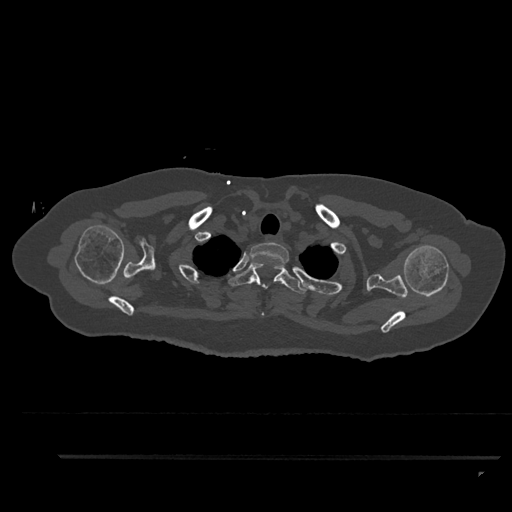
CT including the spine, one axial slice; slice 736 of 797 in the series (ordered by position); 120 kVp; bone window (W 1800 / L 400 HU); 512 × 512 image matrix, field of view 408 × 408 mm. Patient: female, 44 years. Case-level facts recorded for this patient, not image findings: primary cancer: renal.
Annotated regions visible in this slice (semi-automatic segmentation, software-assisted and operator-edited):
- T1 vertebra: bounding box (x1, y1, x2, y2) in pixels: (249, 242, 289, 316)
- T2 vertebra: (228, 262, 307, 294)